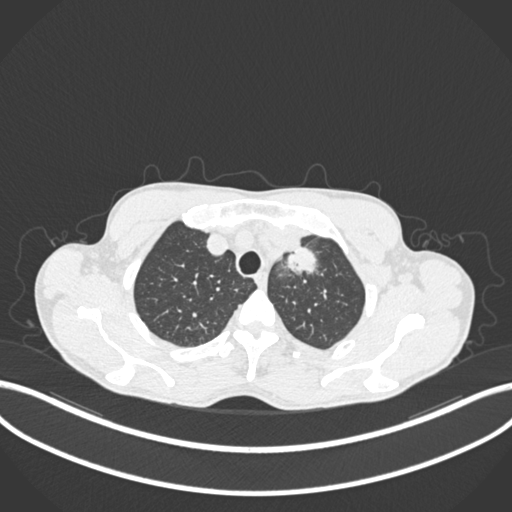
Chest CT, one axial slice. Slice 172 of 211 in the series (ordered by position). Reconstruction kernel B30f. 120 kVp. Lung window (W 1500 / L -600 HU). 512 × 512 image matrix, field of view 400 × 400 mm. Patient: male, 58 years. From the clinical record (not read from this slice): clinical TNM (as recorded): T1c N1 M0.
Outlined on this slice (bounding box drawn by a radiologist):
- lung tumour (recorded histology: adenocarcinoma): bounding box <282,243,318,280> (left, top, right, bottom; pixels)